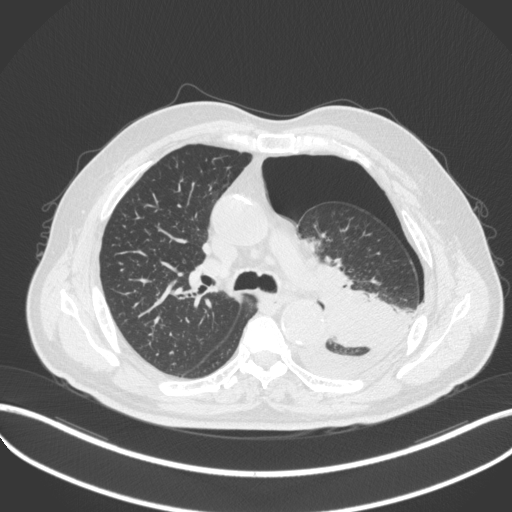
Chest CT, one axial slice. Position 335 of 466 along the scan axis. Lung window (W 1500 / L -600 HU). 512 × 512 image matrix, field of view 400 × 400 mm. Male patient, age 76 years. From the clinical record (not read from this slice): clinical TNM (as recorded): T3 N0 M1b.
Outlined on this slice (rectangle marked by the reading radiologist):
- lung tumour (recorded histology: adenocarcinoma): box from (x=317, y=286) to (x=398, y=350) px